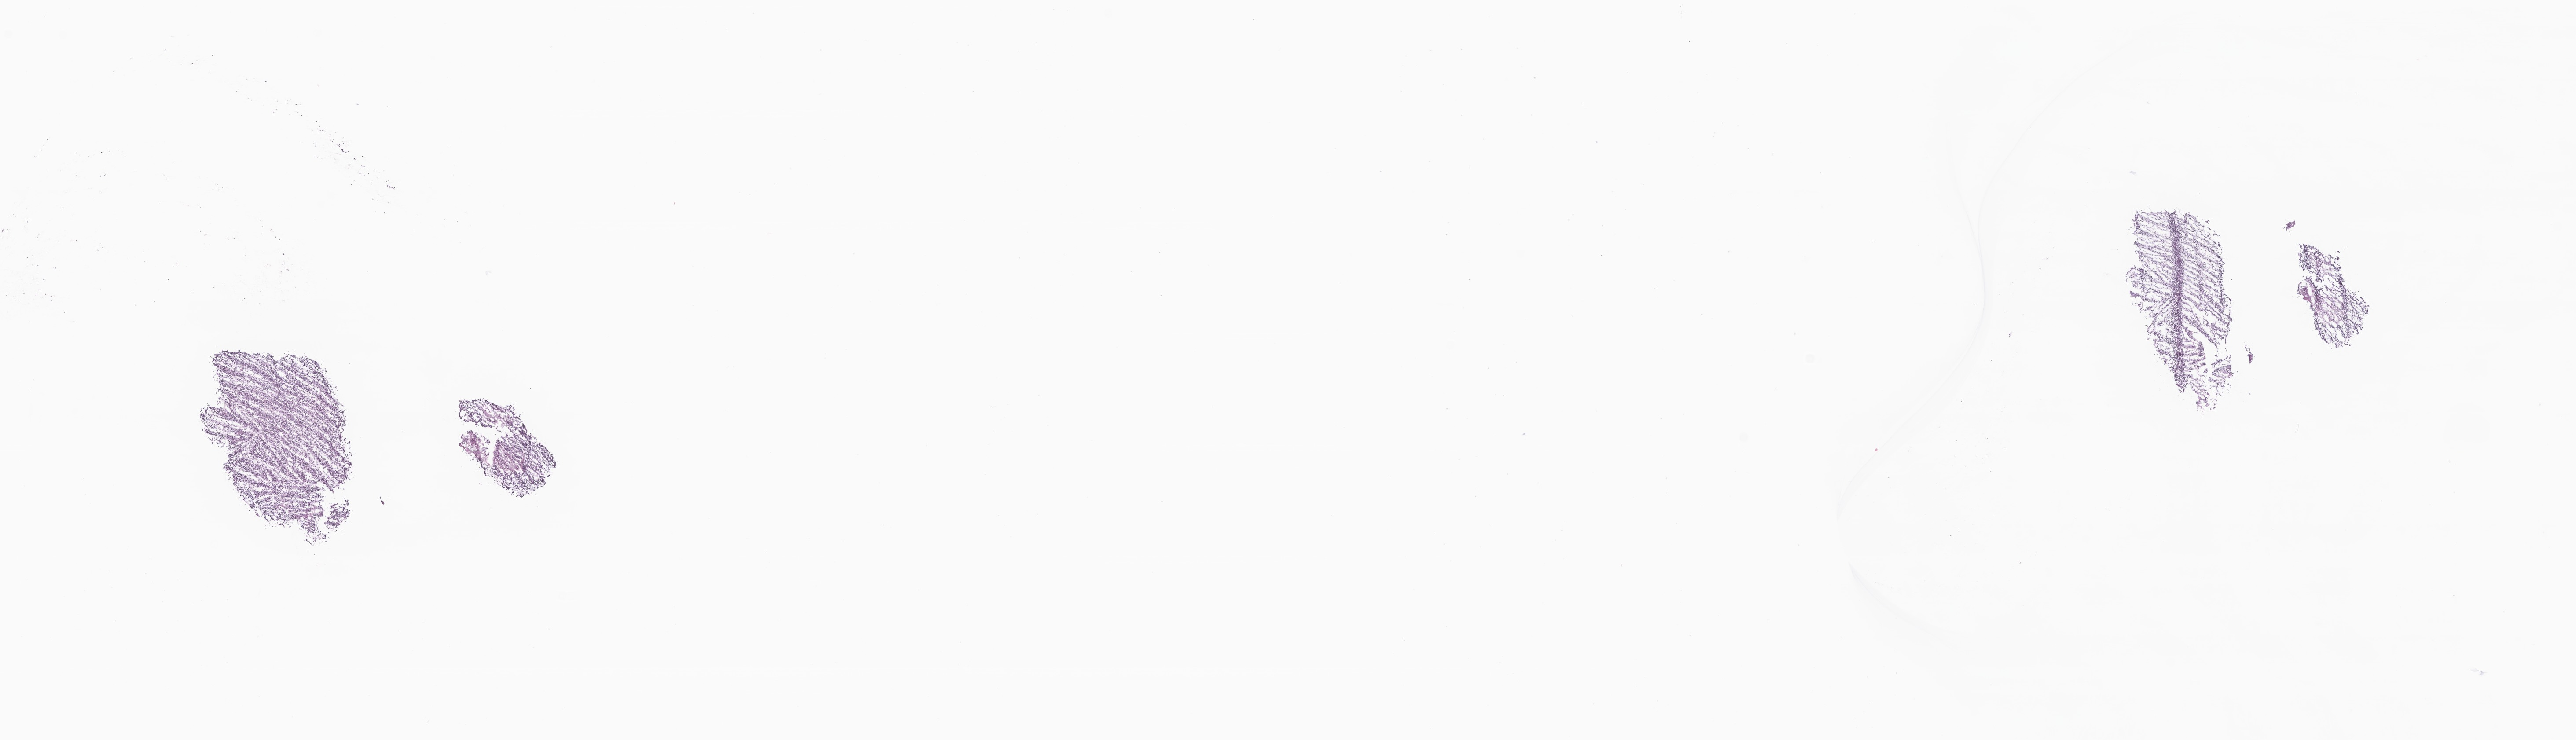
Haematoxylin and eosin whole-slide image of tumor tissue from the cerebellum — low-resolution overview of the scanned area, about 24.7 x 7.1 mm. Frozen section. Patient: male, age 82 months (6 years 10 months).
Diagnosis (ICD-O-3 morphology term): Medulloblastoma, NOS.